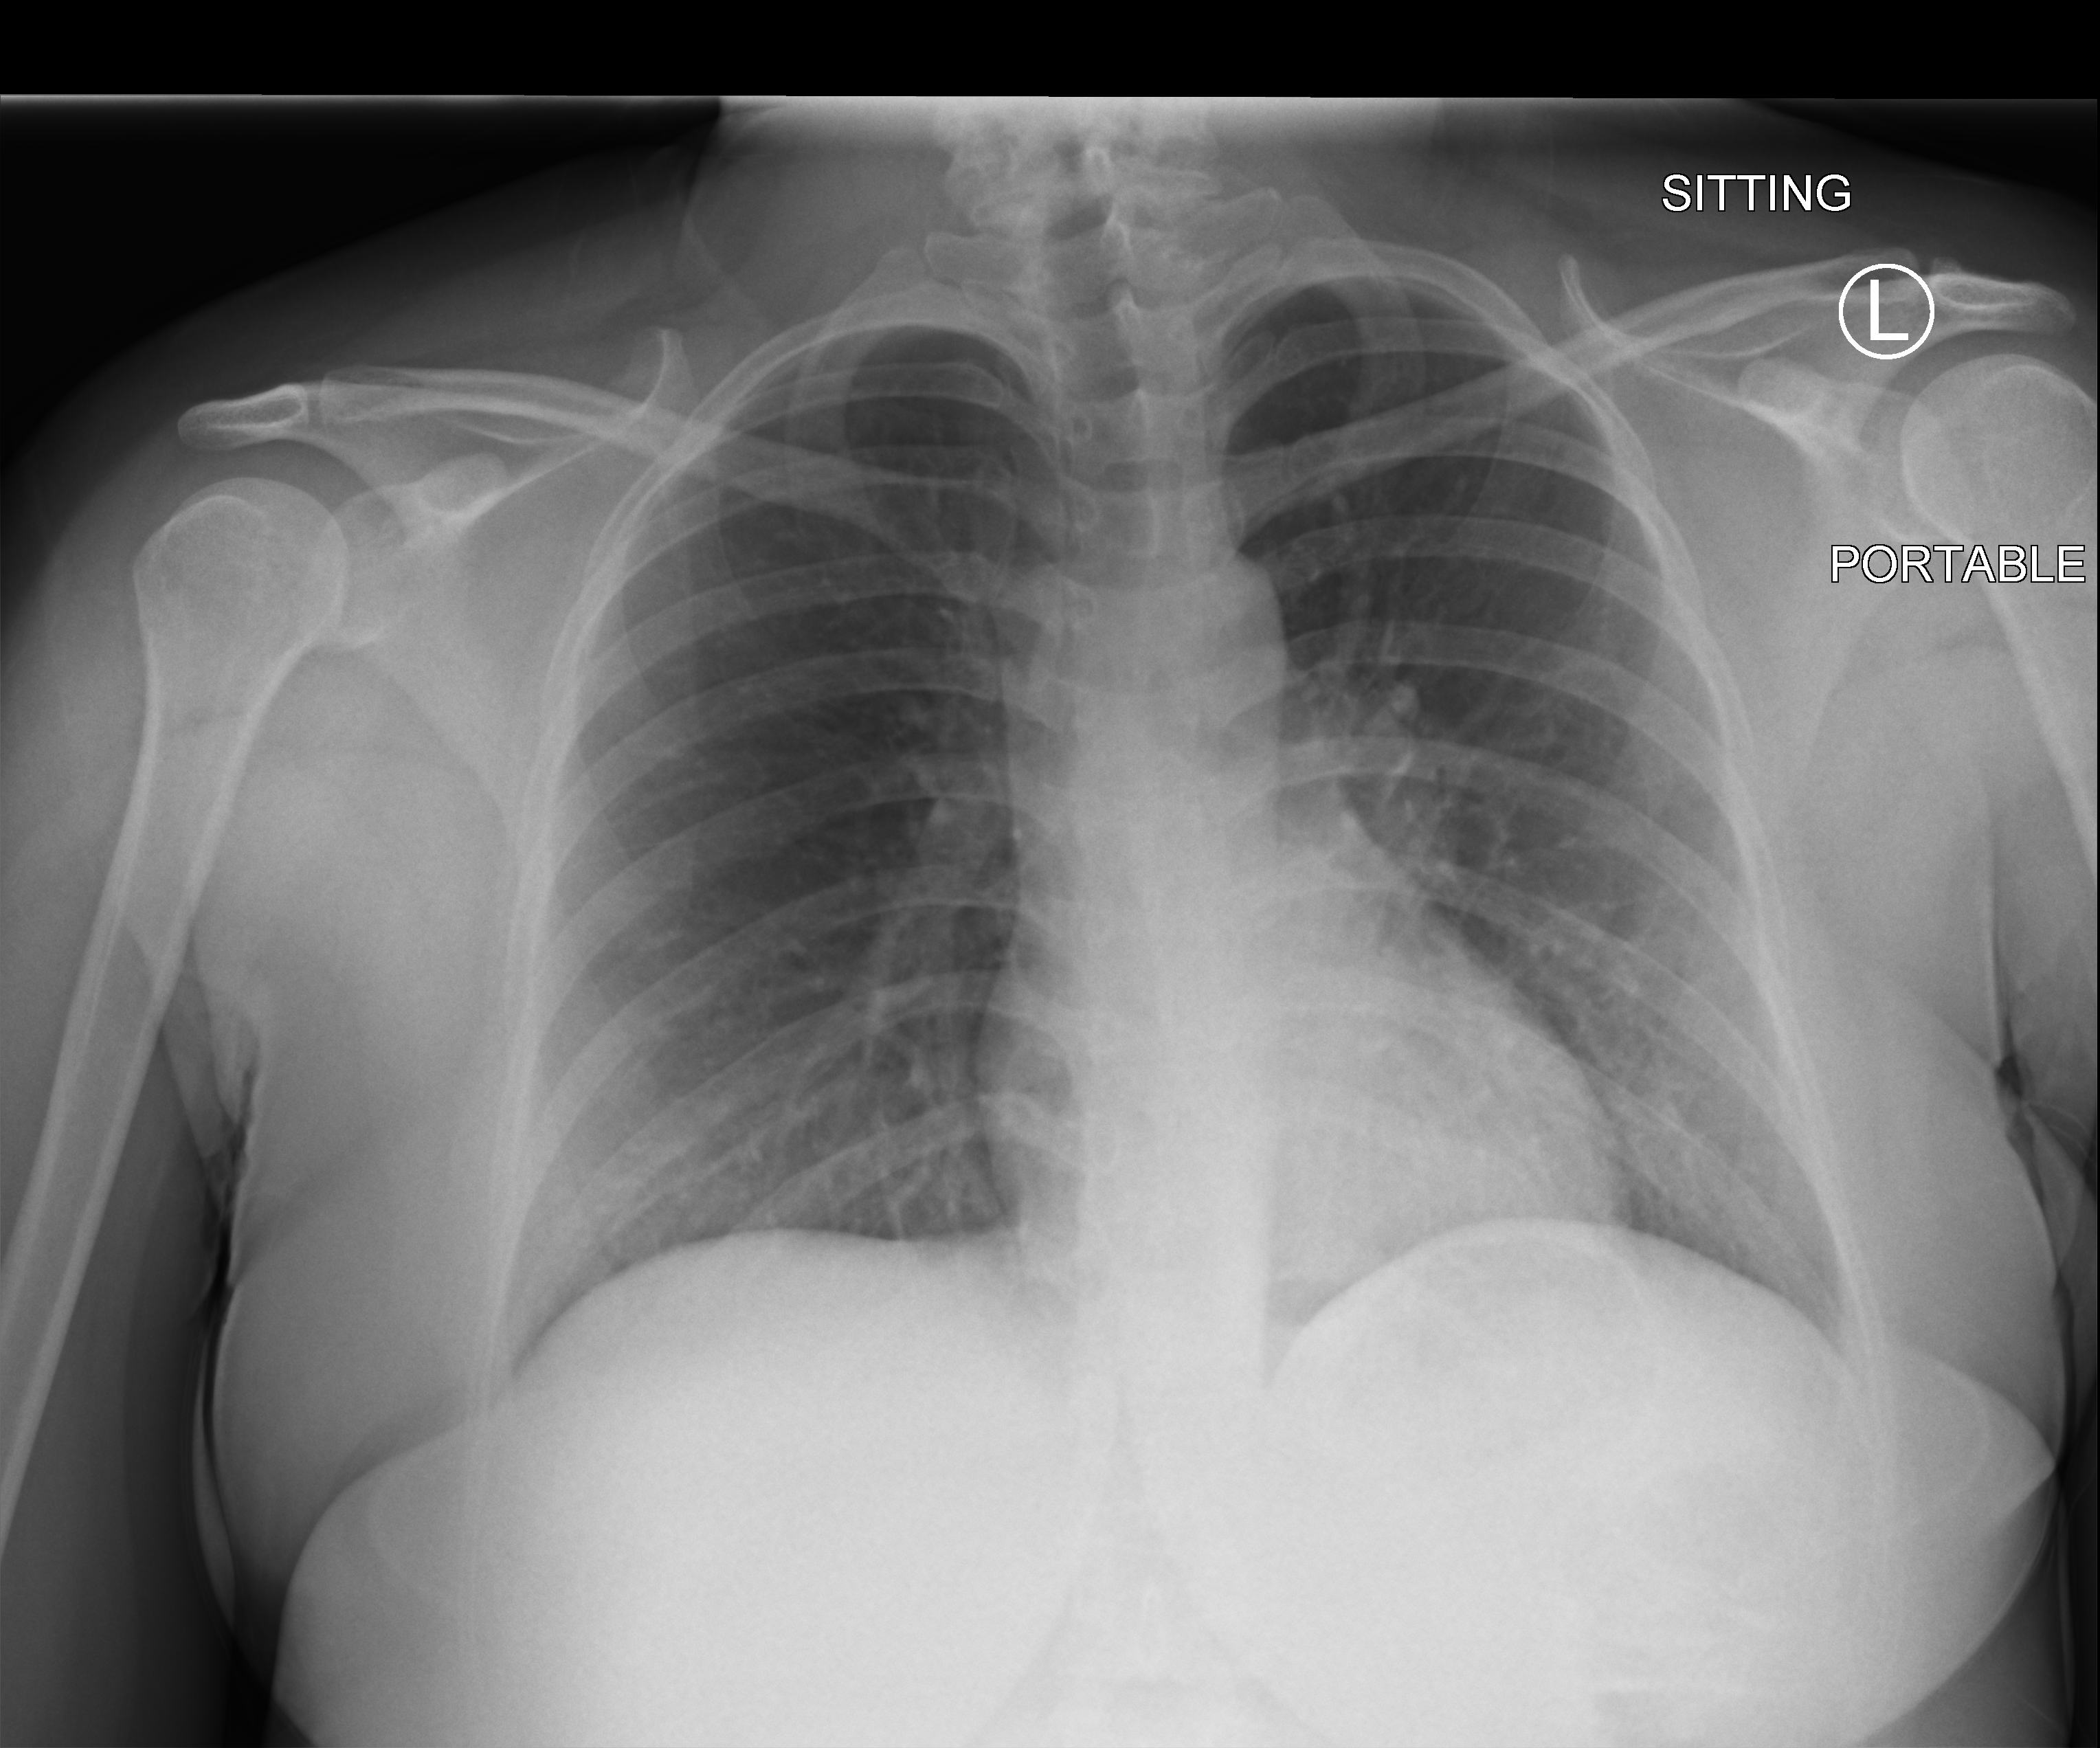
Bedside chest radiograph (computed radiography), anteroposterior (AP) projection. Female patient hospitalised with COVID-19, age 18–59 years.
Hospital-stay facts (about this admission, not read from this image; timing relative to this image not recorded):
- mechanically ventilated during this hospital stay: no
- hypertension (admission record): no